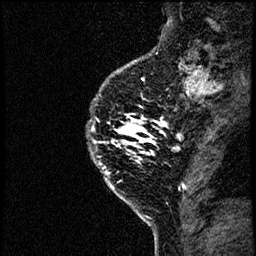
Breast MRI (dynamic contrast-enhanced), one sagittal slice. Slice 52 of 60 in the series (ordered by position). Dynamic contrast-enhanced study with each time point stored as its own series, time point 2 of 4 at this slice position (early post-contrast, ordered by acquisition time). 1.5 T. TE 4.2 ms, TR 17.6 ms. 2 mm slice thickness. 256 × 256 image matrix, field of view 200 × 200 mm. Female patient, age 40 years. From the clinical record (not read from this slice): setting: breast cancer imaged before/during neoadjuvant chemotherapy; receptor status: HER2-positive.
Outlined on this slice (semi-automatic segmentation, software-assisted and operator-edited):
- analysis volume of interest (the breast-tissue region the enhancement analysis was run in; not a lesion): bounding box [x1, y1, x2, y2] px = [81, 55, 185, 206]
- tumour enhancement mask (voxels above the 100 % enhancement threshold inside the analysis volume of interest): [96, 116, 185, 205]